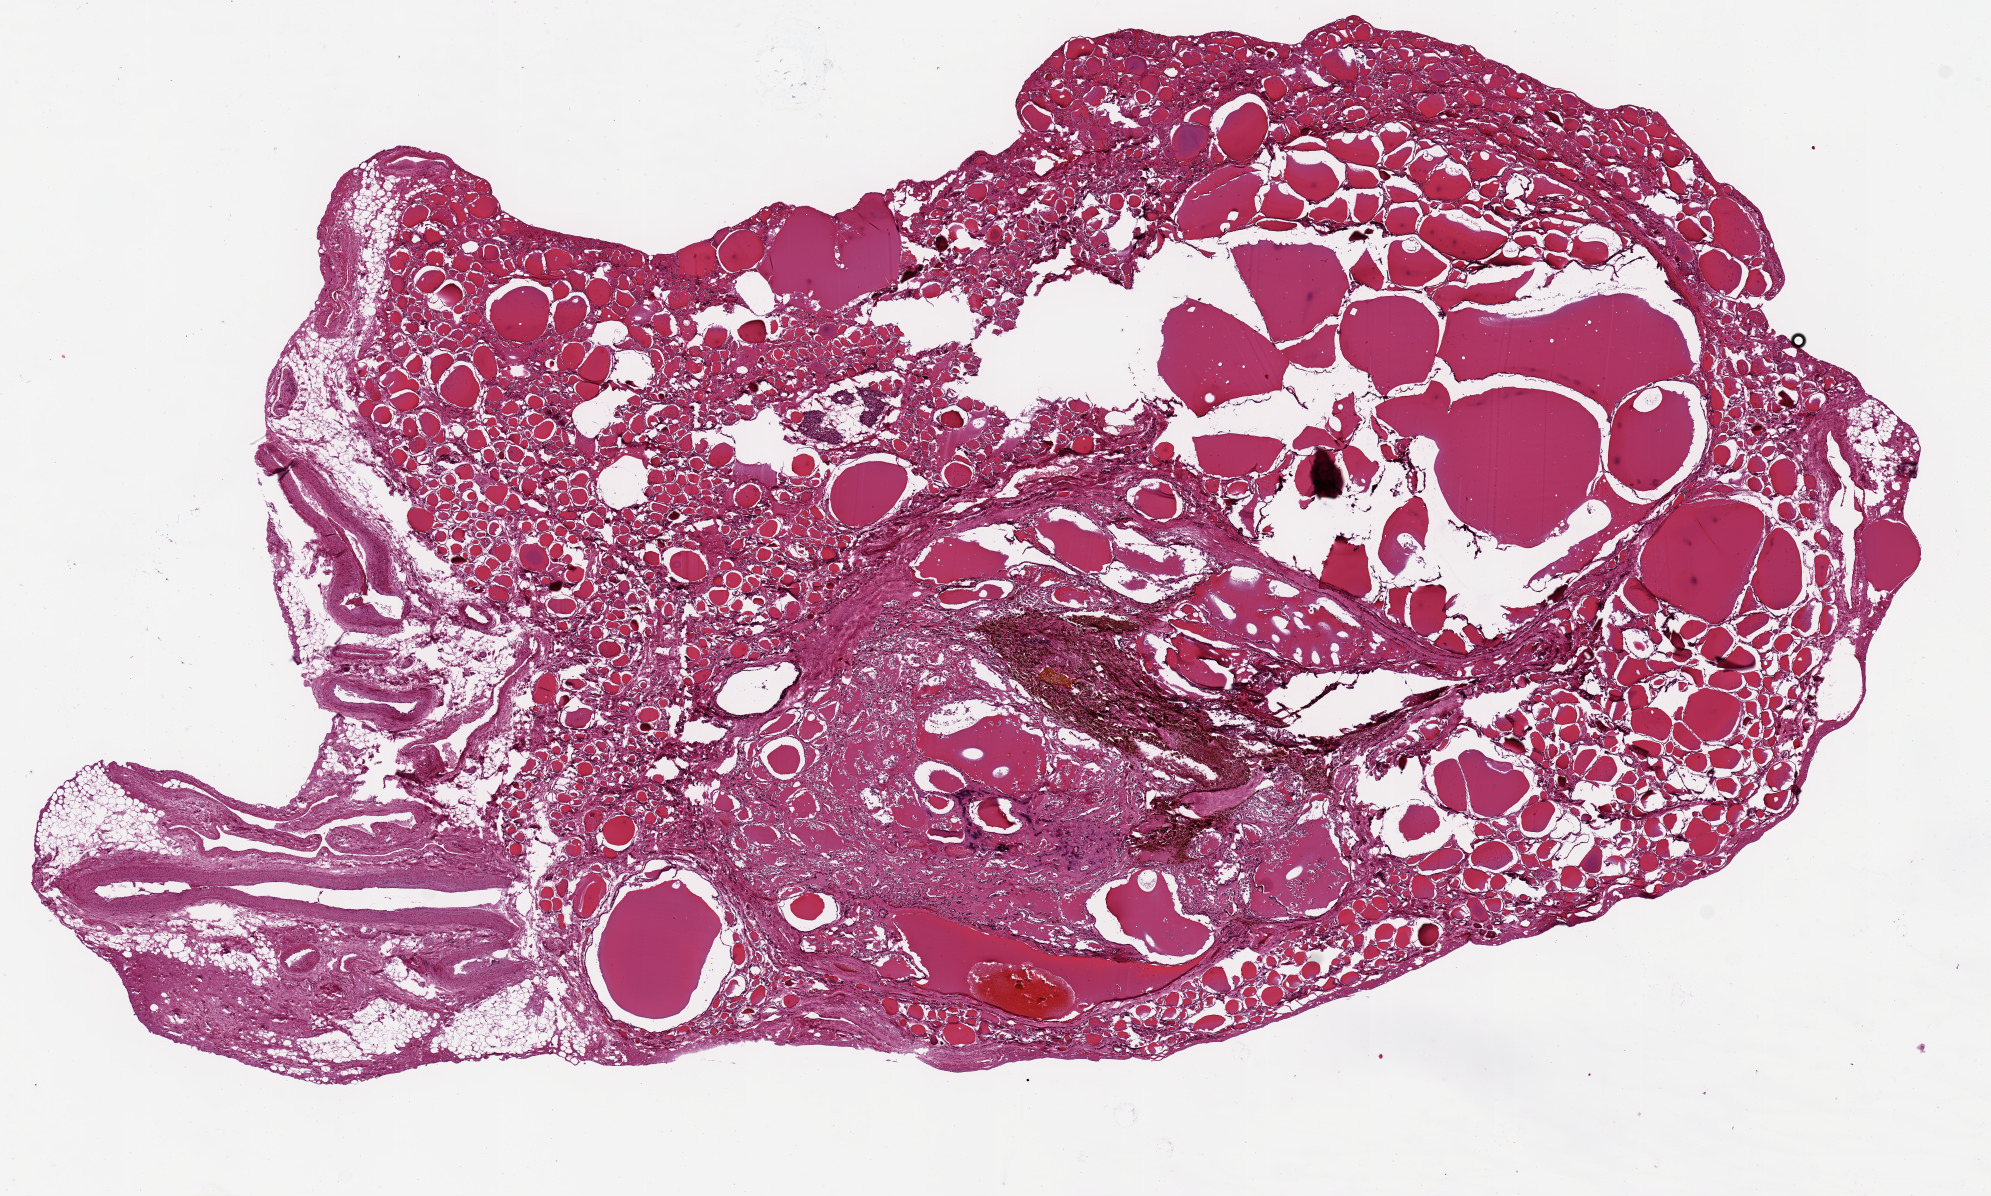
Hematoxylin and eosin (H&E) whole-slide image, brightfield, whole scanned area (about 15.8 x 9.5 mm, acquisition: 20x scan) shown as a low-resolution overview, PAXgene-fixed, paraffin-embedded tissue, section of thyroid (target tissue), tissue donor sample. Female donor.
Reviewer comment on this tissue sample: 3.7x4.5mm colloid nodule in 12 x12mm specimen. Mild autolysis (???score 1???).